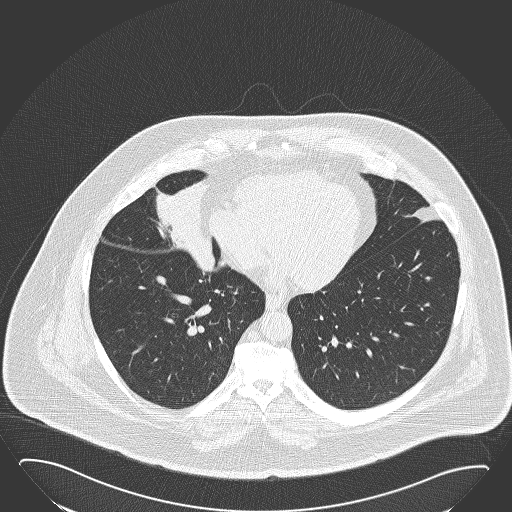
Low-dose screening chest CT, axial slice, first (baseline) screen, lung window (W 1500 / L -600 HU), 2 mm slice thickness, 120 kVp, slice 105 of 168 in the series, 512 × 512 image matrix. Male participant, aged 61 years at enrolment.
- Lesion marked by an expert reader, bounding box (x1, y1, x2, y2) in pixels: (132, 169, 227, 259).
- The screening reader recorded 2 non-calcified nodules or masses ≥4 mm on this exam (right middle lobe, left lower lobe); which of them this box marks is not recorded.
- Official screen result: positive, change unspecified: nodule(s) >= 4 mm or enlarging nodule(s), mass(es), or other non-specific abnormalities suspicious for lung cancer.
- Lung cancer was diagnosed 47 days after this screen: basaloid squamous cell carcinoma, right middle lobe, right hilum, poorly differentiated (G3), stage IIB (AJCC 6th edition), 95 mm at pathology.